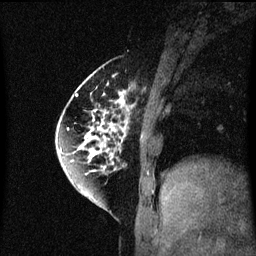
Breast MRI (dynamic contrast-enhanced), one sagittal slice. Position 18 of 60 along the scan axis. Dynamic contrast-enhanced series, image 2 of 3 at this slice position (ordered by acquisition). 1.5 T. TE 4.2 ms, TR 8.4 ms. 2 mm slice thickness. 256 × 256 image matrix, field of view 200 × 200 mm. Patient: female, 60 years.
Outlined on this slice (semi-automatic segmentation, software-assisted and operator-edited):
- analysis volume of interest (the breast-tissue region the enhancement analysis was run in; not a lesion): bounding box <64,70,131,195> (left, top, right, bottom; pixels)
- tumour enhancement mask (voxels above the 70 % enhancement threshold inside the analysis volume of interest): <64,72,131,195>